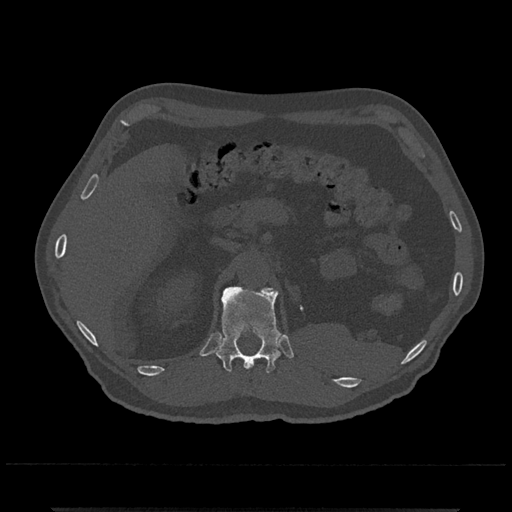
CT including the spine, one axial slice; position 432 of 797 along the scan axis; 120 kVp; bone window (W 1800 / L 400 HU); 0.5 mm slice thickness; 512 × 512 image matrix, field of view 393 × 393 mm. Patient: male, 67 years. Case-level facts recorded for this patient, not image findings: primary cancer: prostate.
Annotated regions visible in this slice (semi-automatically segmented with operator editing):
- T12 vertebra: bounding box <214,286,281,373> (left, top, right, bottom; pixels)